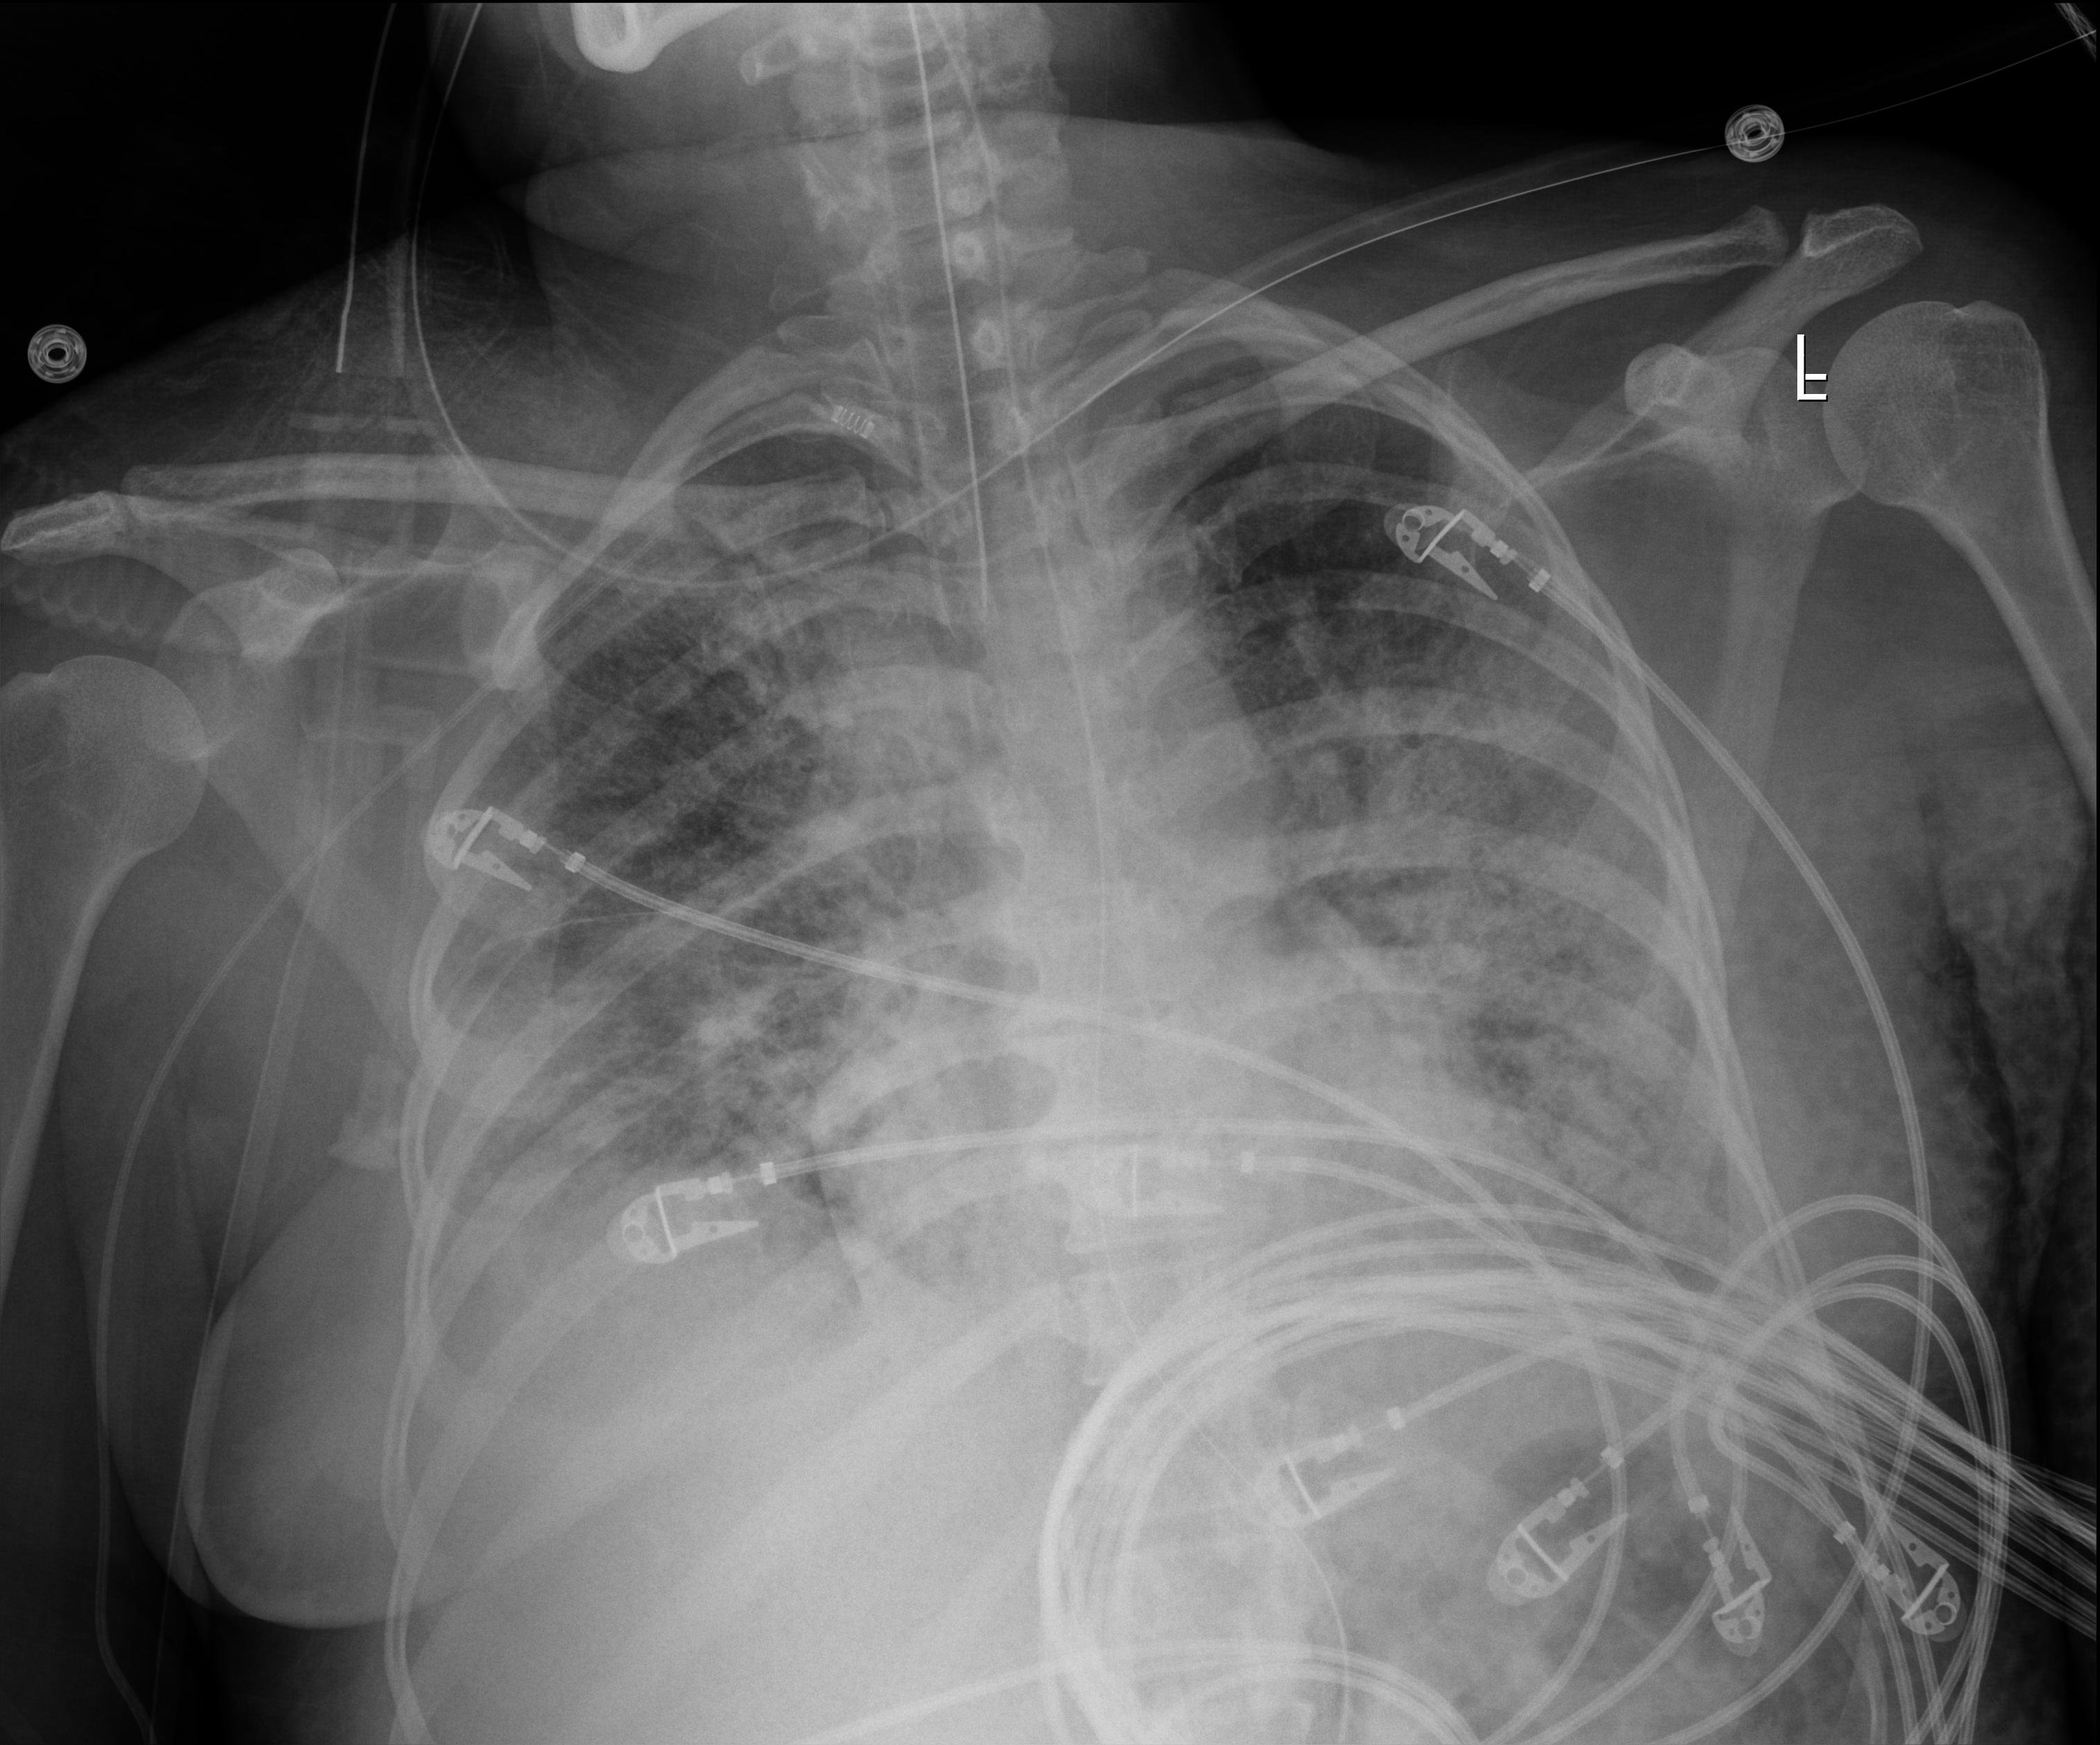
Chest radiograph, anteroposterior (AP) projection. Female patient hospitalised with COVID-19, age 18–59 years.
Hospital-stay facts (about this admission, not read from this image; timing relative to this image not recorded): admitted to intensive care during this hospital stay: yes.